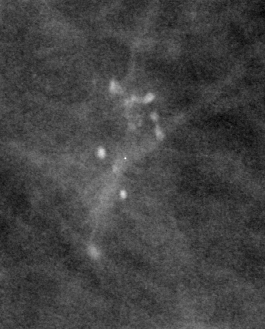
Crop from a digitized film mammogram around one marked abnormality, left breast, CC view.
Marked abnormality: calcifications, morphology pleomorphic / pleomorphic, distribution regional / regional; BI-RADS assessment category 4; pathology (as recorded): benign.